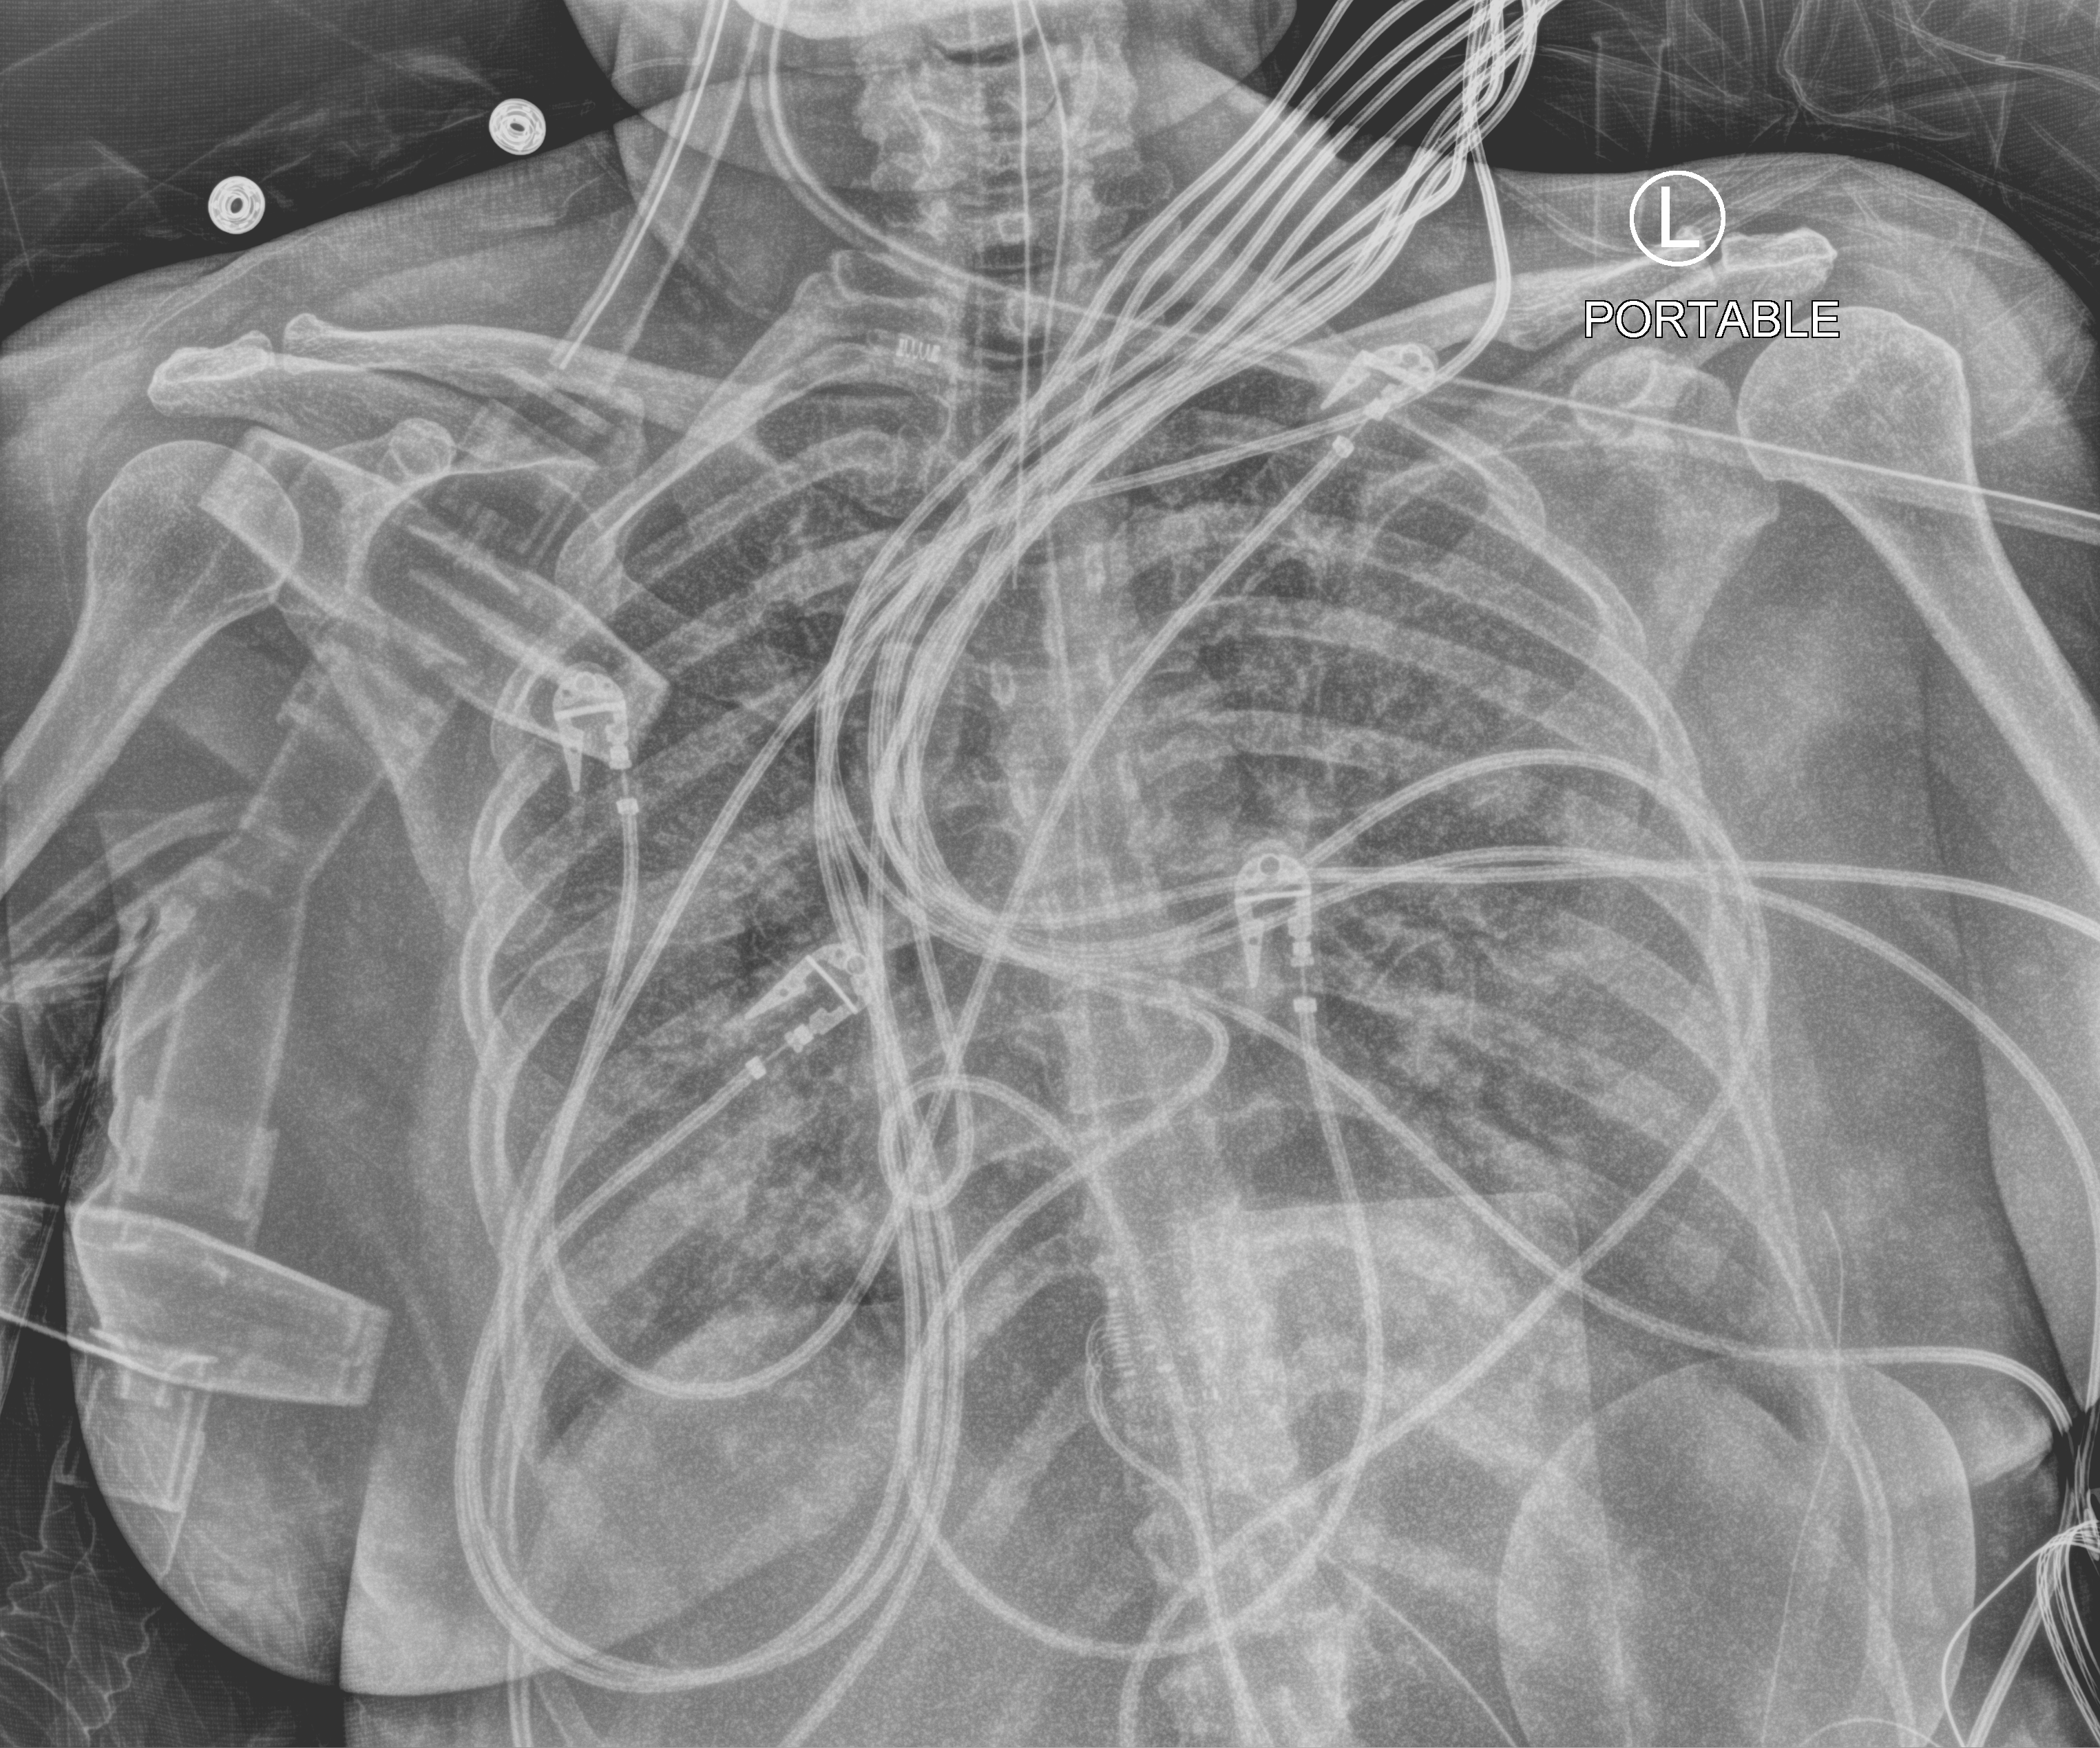
Portable chest radiograph, anteroposterior (AP) projection. Patient hospitalised with COVID-19; male, aged 18–59 years.
From the hospital-stay record, not from the radiograph (when in the stay this image was taken is not recorded):
- smoking status (admission record): never